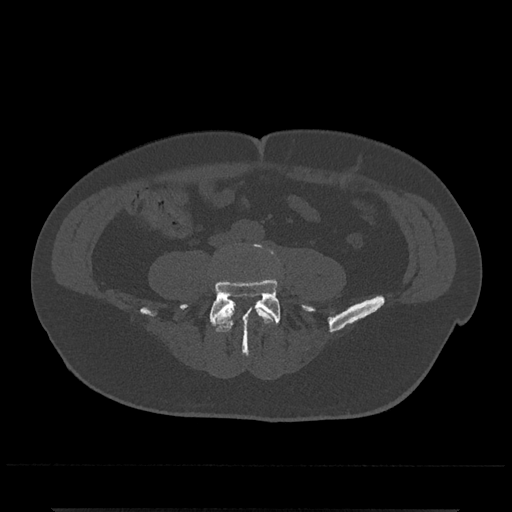
CT including the spine, one axial slice. Position 110 of 797 along the scan axis. Reconstruction kernel Br40s/3. 120 kVp. Bone window (W 1800 / L 400 HU). 0.5 mm slice thickness. 512 × 512 image matrix, field of view 393 × 393 mm. Male patient, age 67 years. Case-level facts recorded for this patient, not image findings: primary cancer: prostate.
Structures marked on this image (semi-automatically segmented with operator editing):
- L4 vertebra: box from (x=213, y=302) to (x=277, y=332) px
- L5 vertebra: (x=181, y=243)–(x=314, y=354)